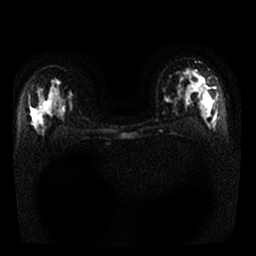
Breast MRI, one axial slice. Position 18 of 25 along the scan axis. Diffusion-weighted series; image 2 of 4 stored at this slice position (different b-values; order by instance number). 1.5 T. 4 mm slice thickness. 256 × 256 image matrix. Female patient.
Structures marked on this image (expert manual segmentation):
- tumour on diffusion-weighted imaging: bounding box <196,73,211,98> (left, top, right, bottom; pixels)